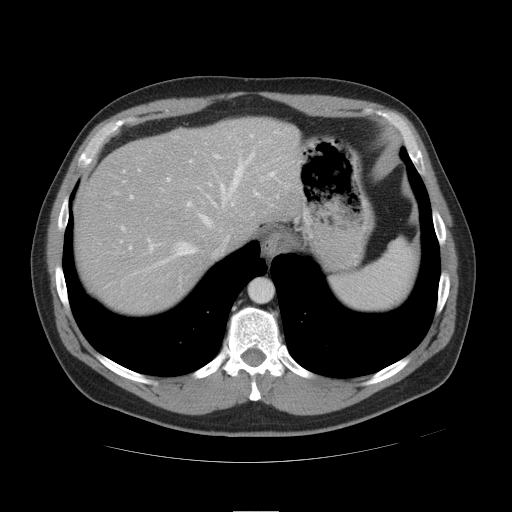
Contrast-enhanced abdominal CT, one axial slice. Position 38 of 49 along the scan axis. Reconstruction kernel STANDARD. 120 kVp. Intravenous contrast given. Soft-tissue window (W 400 / L 40 HU). 512 × 512 image matrix. Male patient, age 52 years. From the clinical record (not read from this slice): diagnosis: colorectal cancer liver metastases, imaged before liver resection; multiple liver metastases: yes; largest metastasis: 5.1 cm; disease in both lobes: yes.
Outlined on this slice (expert manual segmentation):
- hepatic veins: bounding box (x1, y1, x2, y2) in pixels: (129, 141, 262, 265)
- liver: (78, 121, 296, 312)
- planned liver remnant (the part of the liver to remain after resection): (133, 121, 296, 241)
- portal vein (with intrahepatic branches): (120, 134, 272, 253)